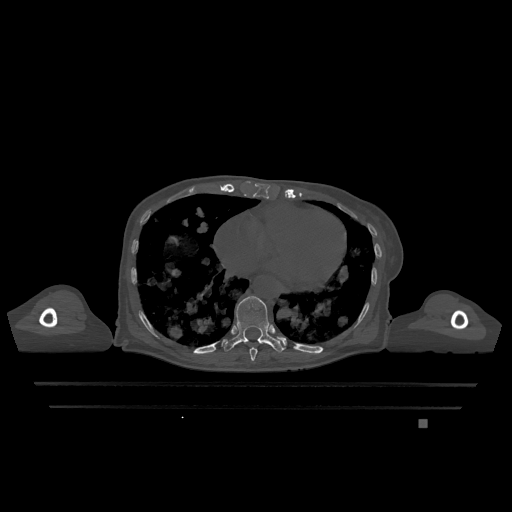
CT including the spine, one axial slice. Slice 658 of 1317 in the series (ordered by position). Bone window (W 1800 / L 400 HU). 0.5 mm slice thickness. 512 × 512 image matrix, field of view 500 × 500 mm. Female patient, age 74 years. Case-level facts recorded for this patient, not image findings: primary cancer: lung.
Outlined on this slice (semi-automatic segmentation, software-assisted and operator-edited):
- T10 vertebra: bounding box [x1, y1, x2, y2] px = [223, 296, 284, 353]
- T9 vertebra: [249, 347, 258, 361]